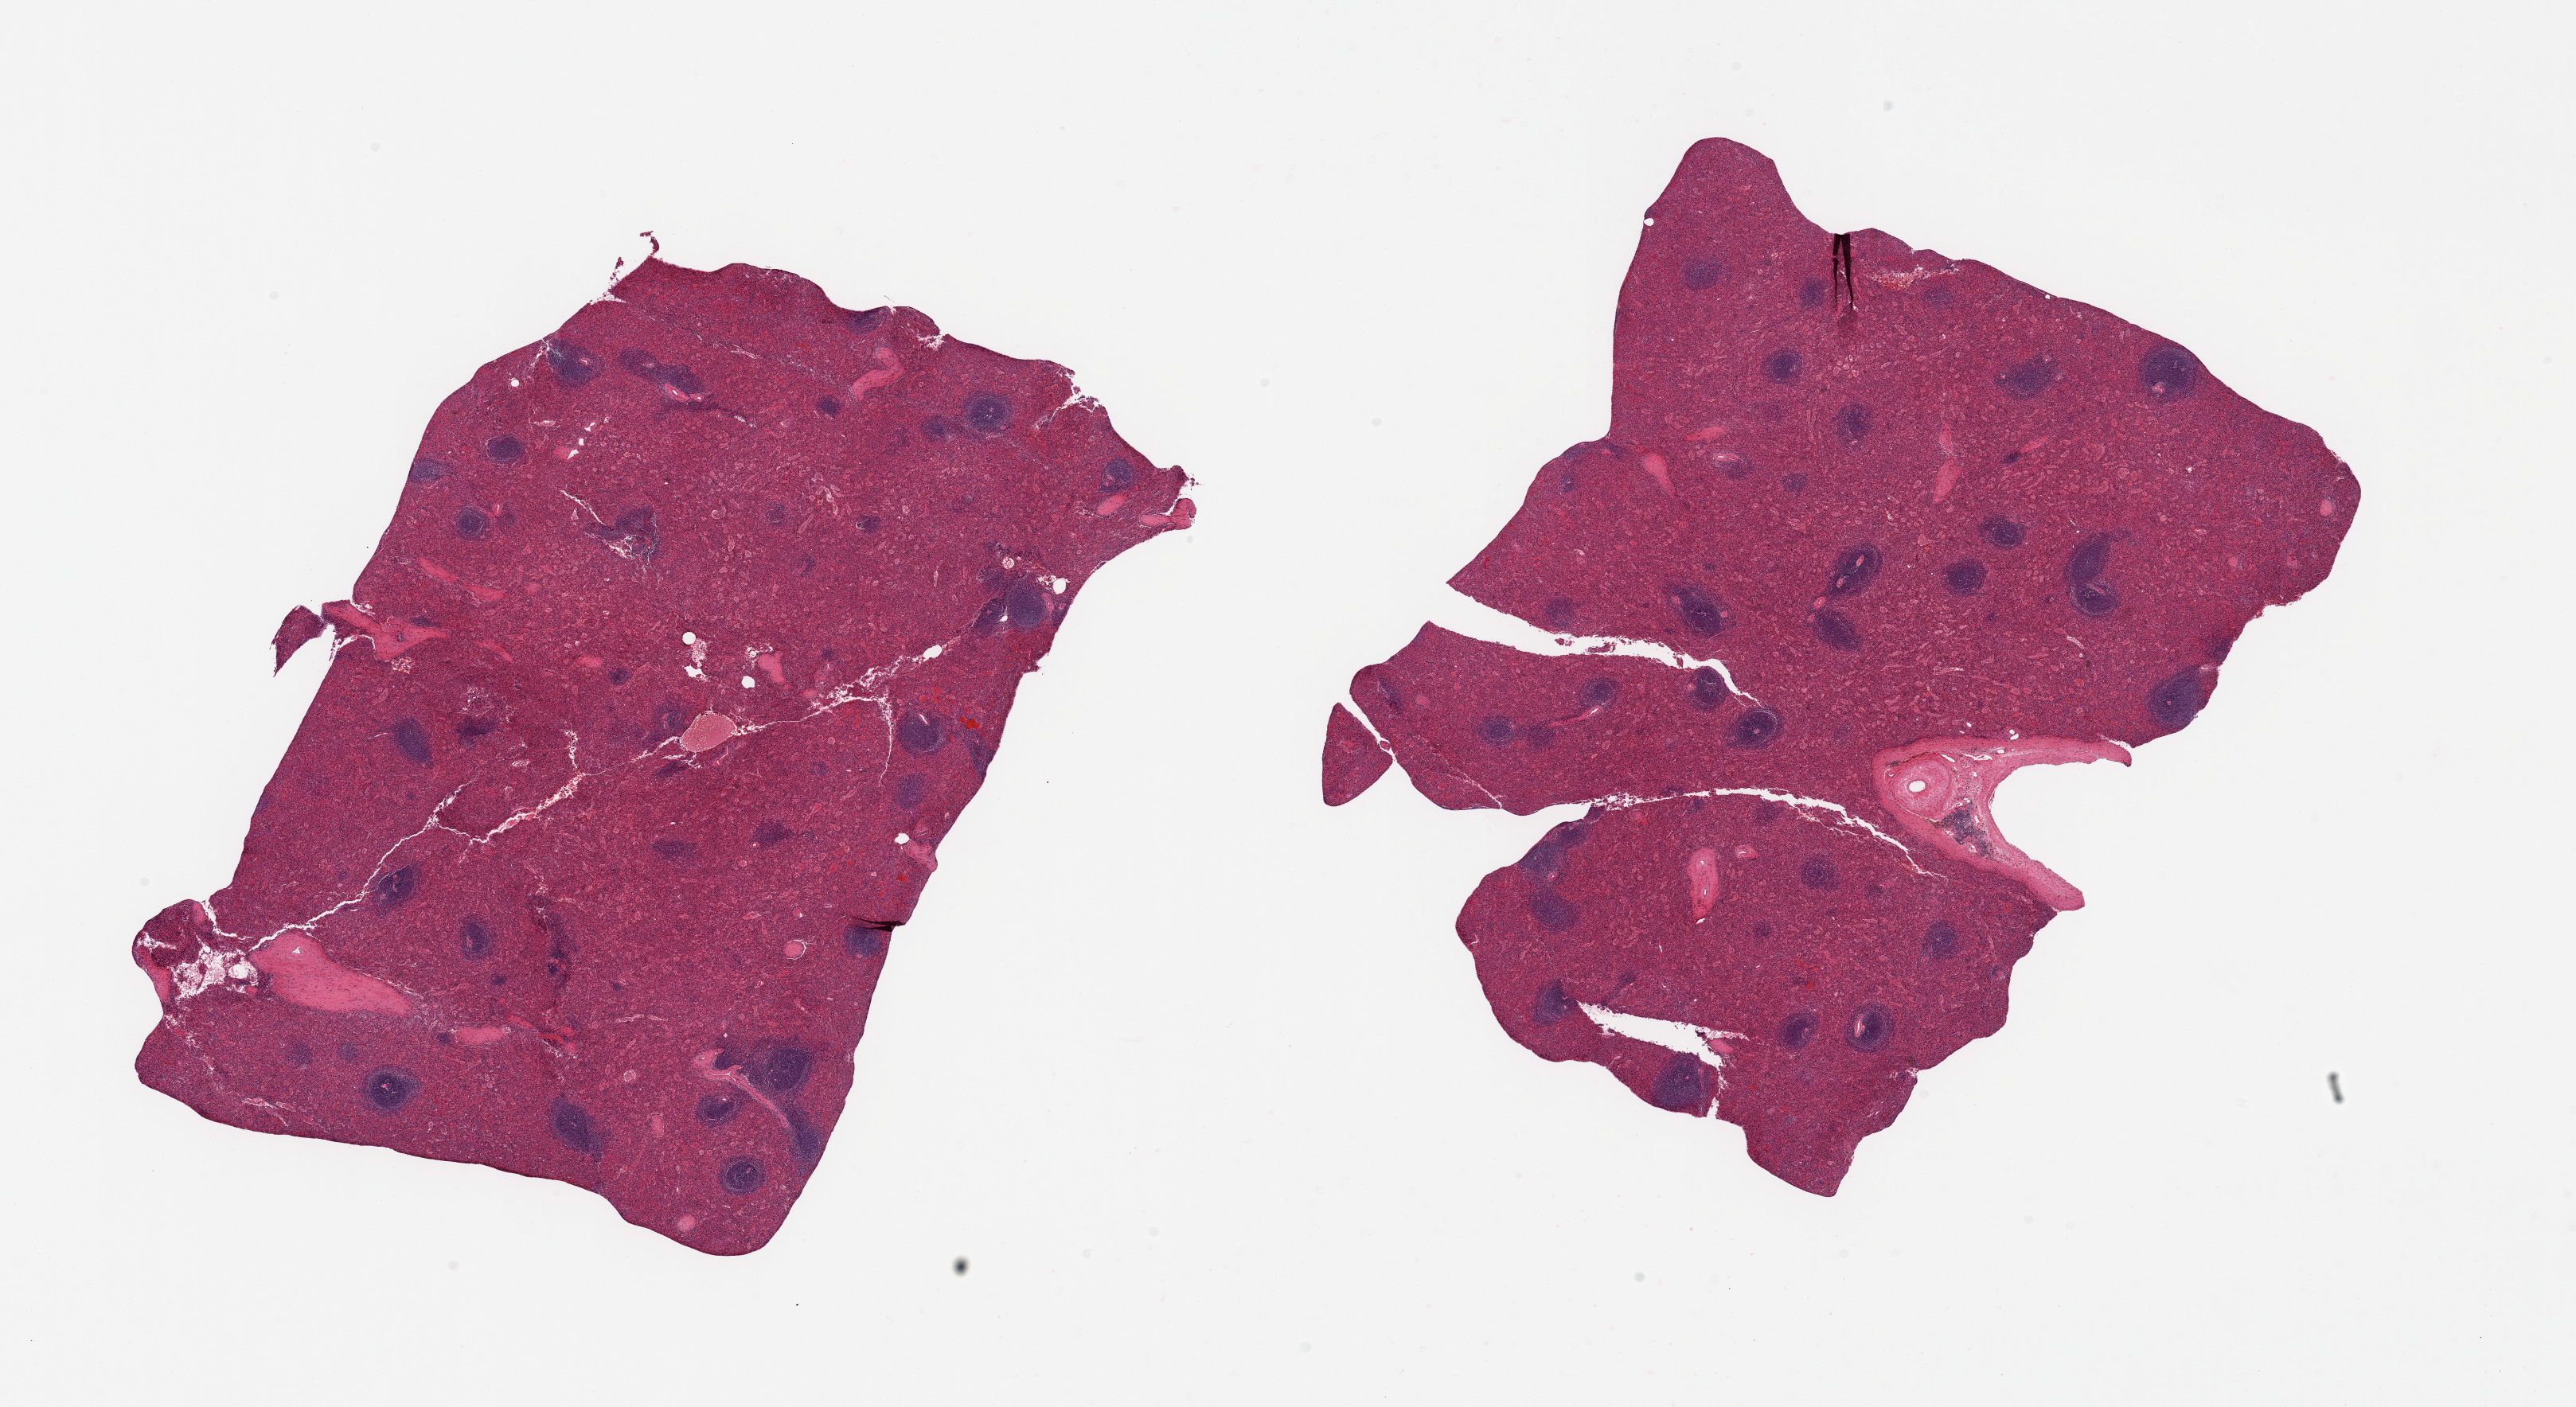
H&E whole-slide image, brightfield — low-resolution overview of the scanned area, about 25.6 x 14.0 mm, PAXgene-fixed, paraffin-embedded tissue, target tissue: spleen, tissue donor sample. Male donor.
Reviewer comment on this tissue sample: 2 pieces; mild congestion.